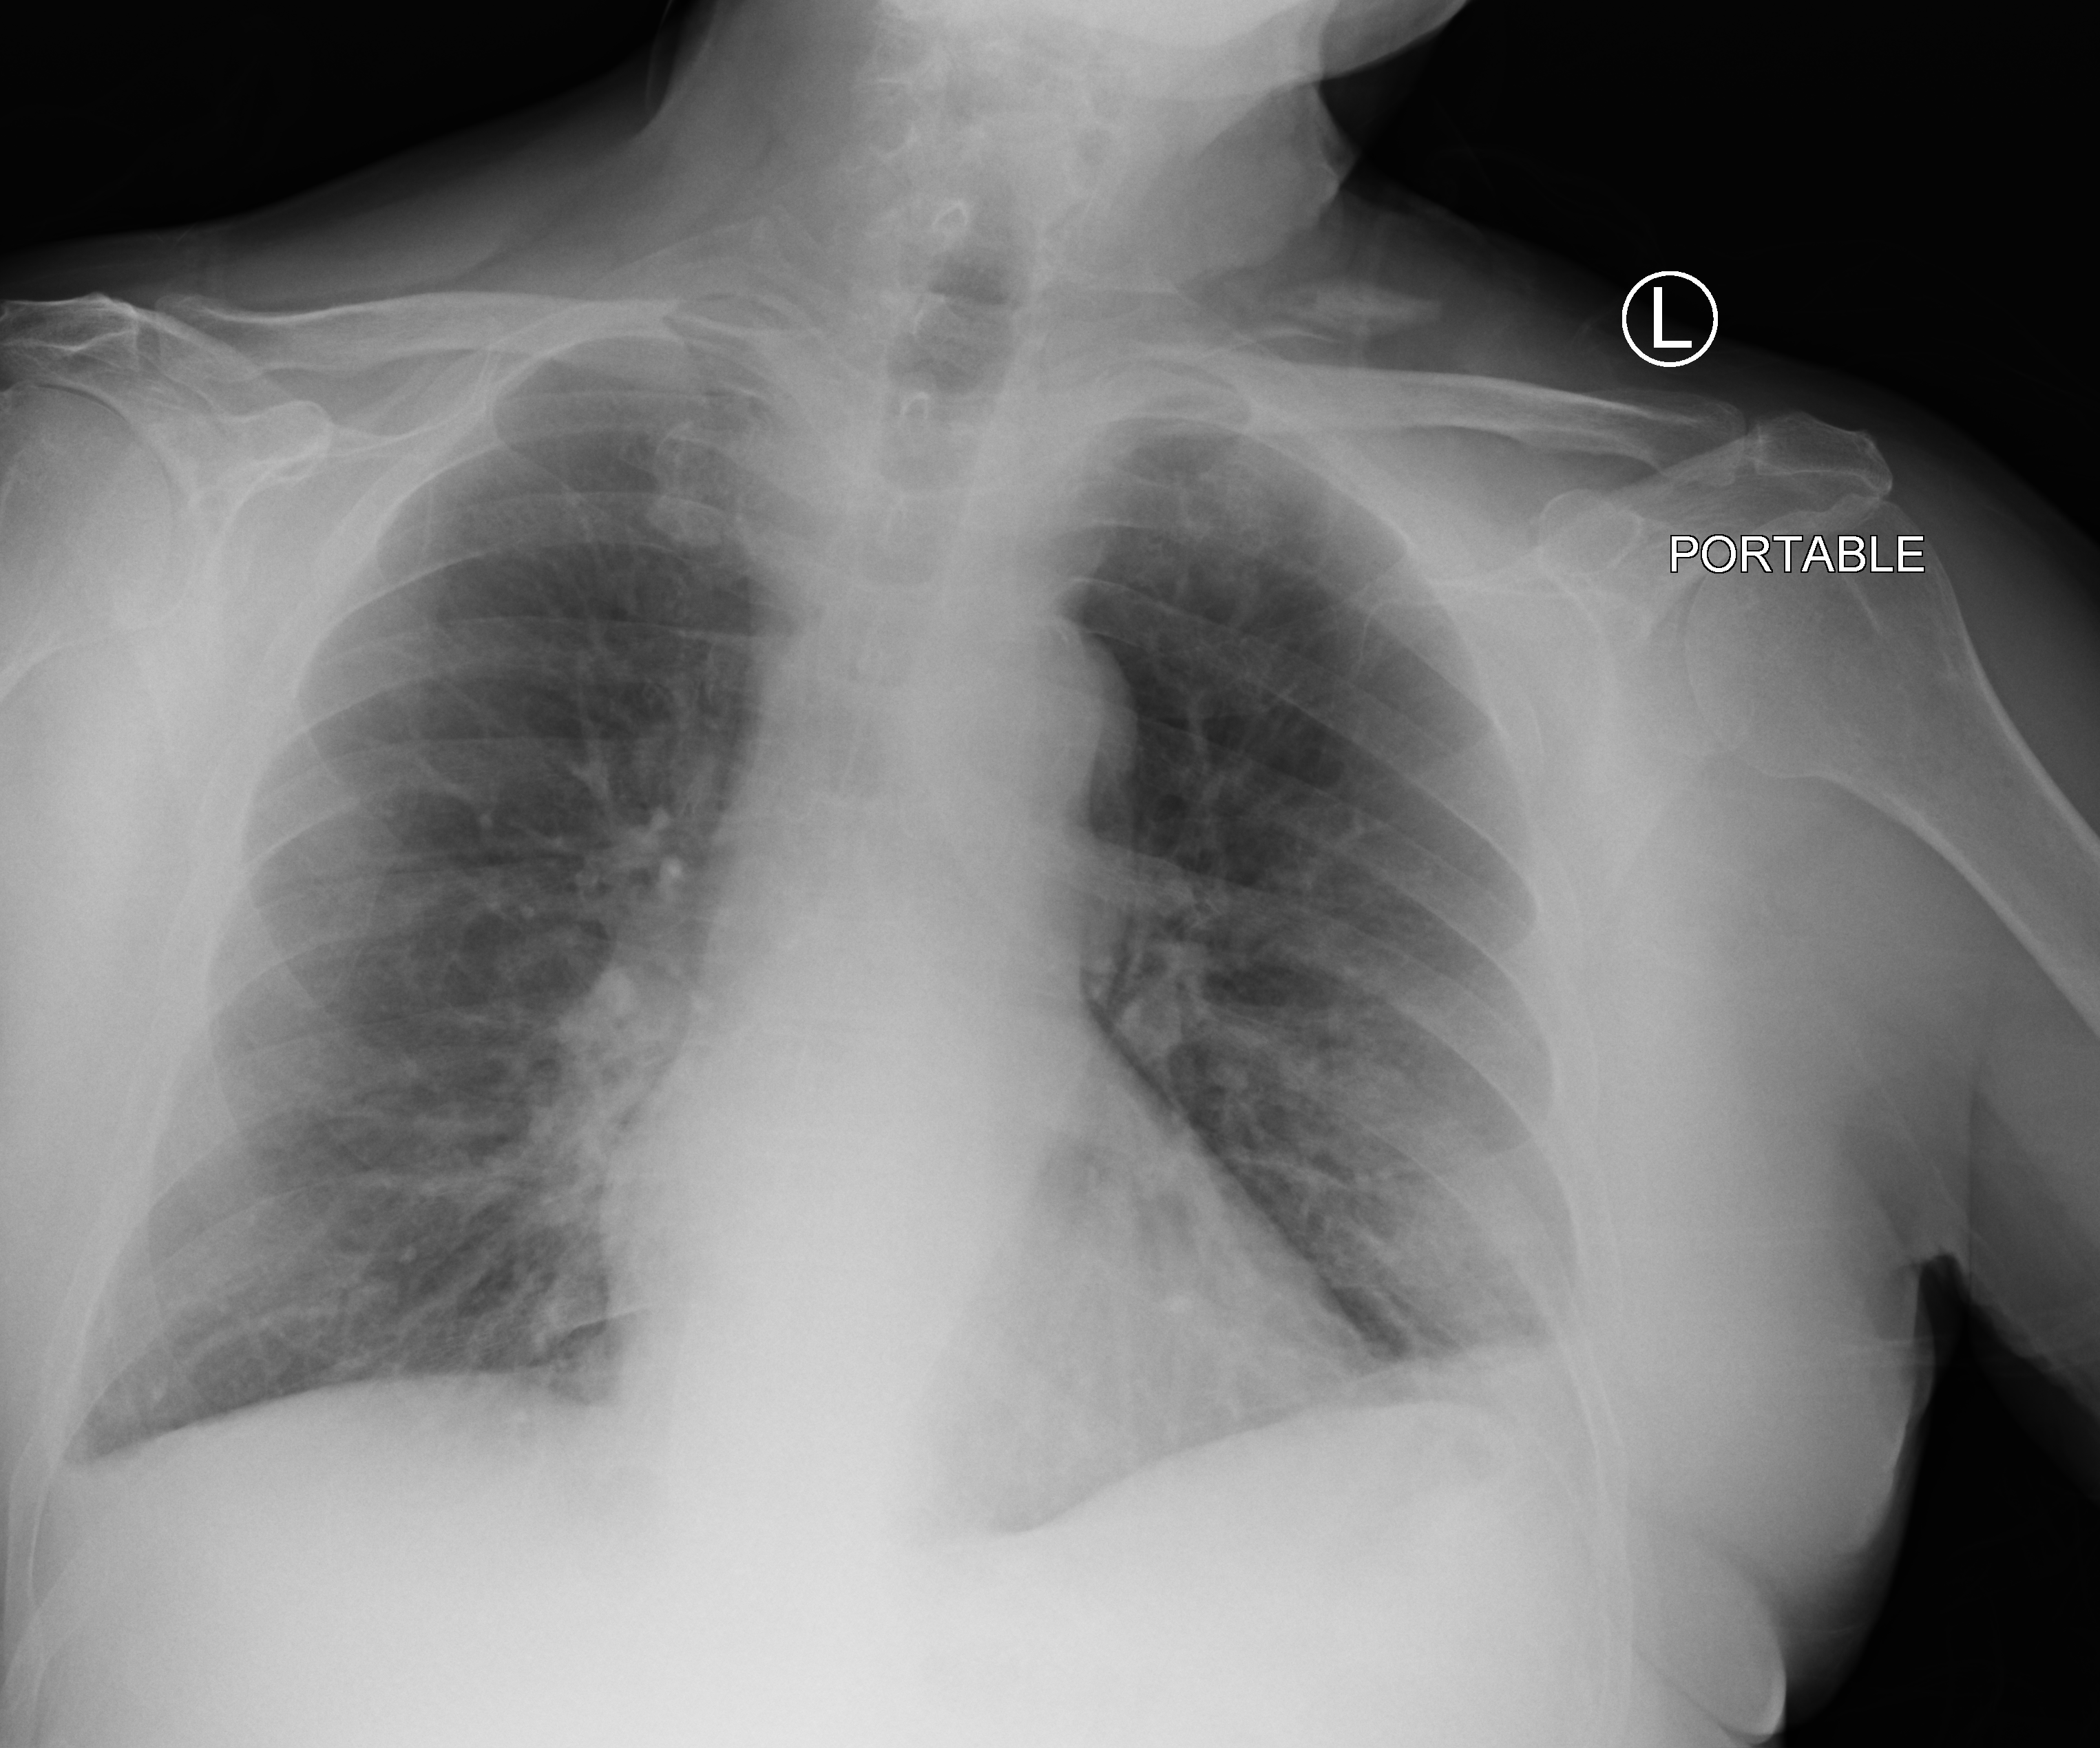
Portable chest radiograph. Patient hospitalised with COVID-19; male, aged 75–90 years.
Admission-level facts for this patient (not findings on this image; timing relative to this image not recorded):
- smoking status (admission record): former